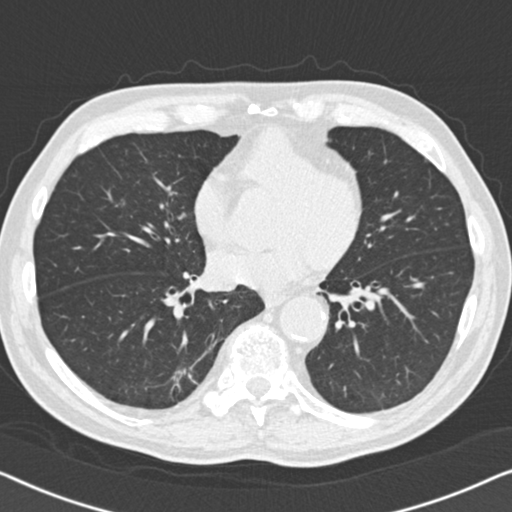
Low-dose screening chest CT, one axial slice. Position 60 of 164 along the scan axis. Reconstruction kernel B30f. 120 kVp. Lung window (W 1500 / L -600 HU). 2 mm slice thickness. 512 × 512 image matrix.
Annotated regions visible in this slice (expert manual segmentation):
- lesion 1 (tumor, lower lobe of right lung): bounding box [x1, y1, x2, y2] px = [171, 369, 186, 382]